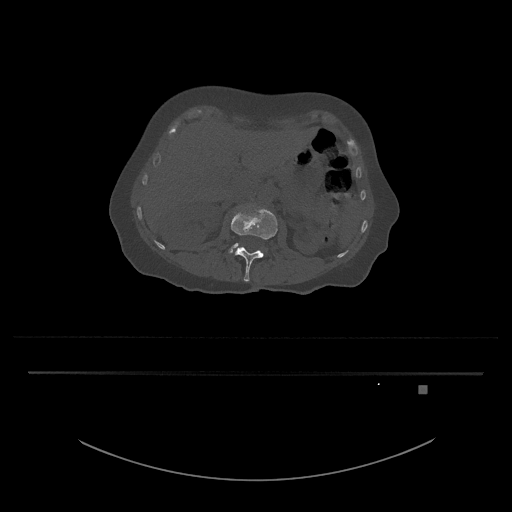
CT including the spine, one axial slice; slice 479 of 797 in the series (ordered by position); reconstruction kernel Br40s/3; bone window (W 1800 / L 400 HU); 0.5 mm slice thickness; 512 × 512 image matrix, field of view 500 × 500 mm. Patient: female, 57 years. Case-level facts recorded for this patient, not image findings: primary cancer: cervical.
Outlined on this slice (semi-automatically segmented with operator editing):
- L3 vertebra: bounding box <228,243,240,254> (left, top, right, bottom; pixels)